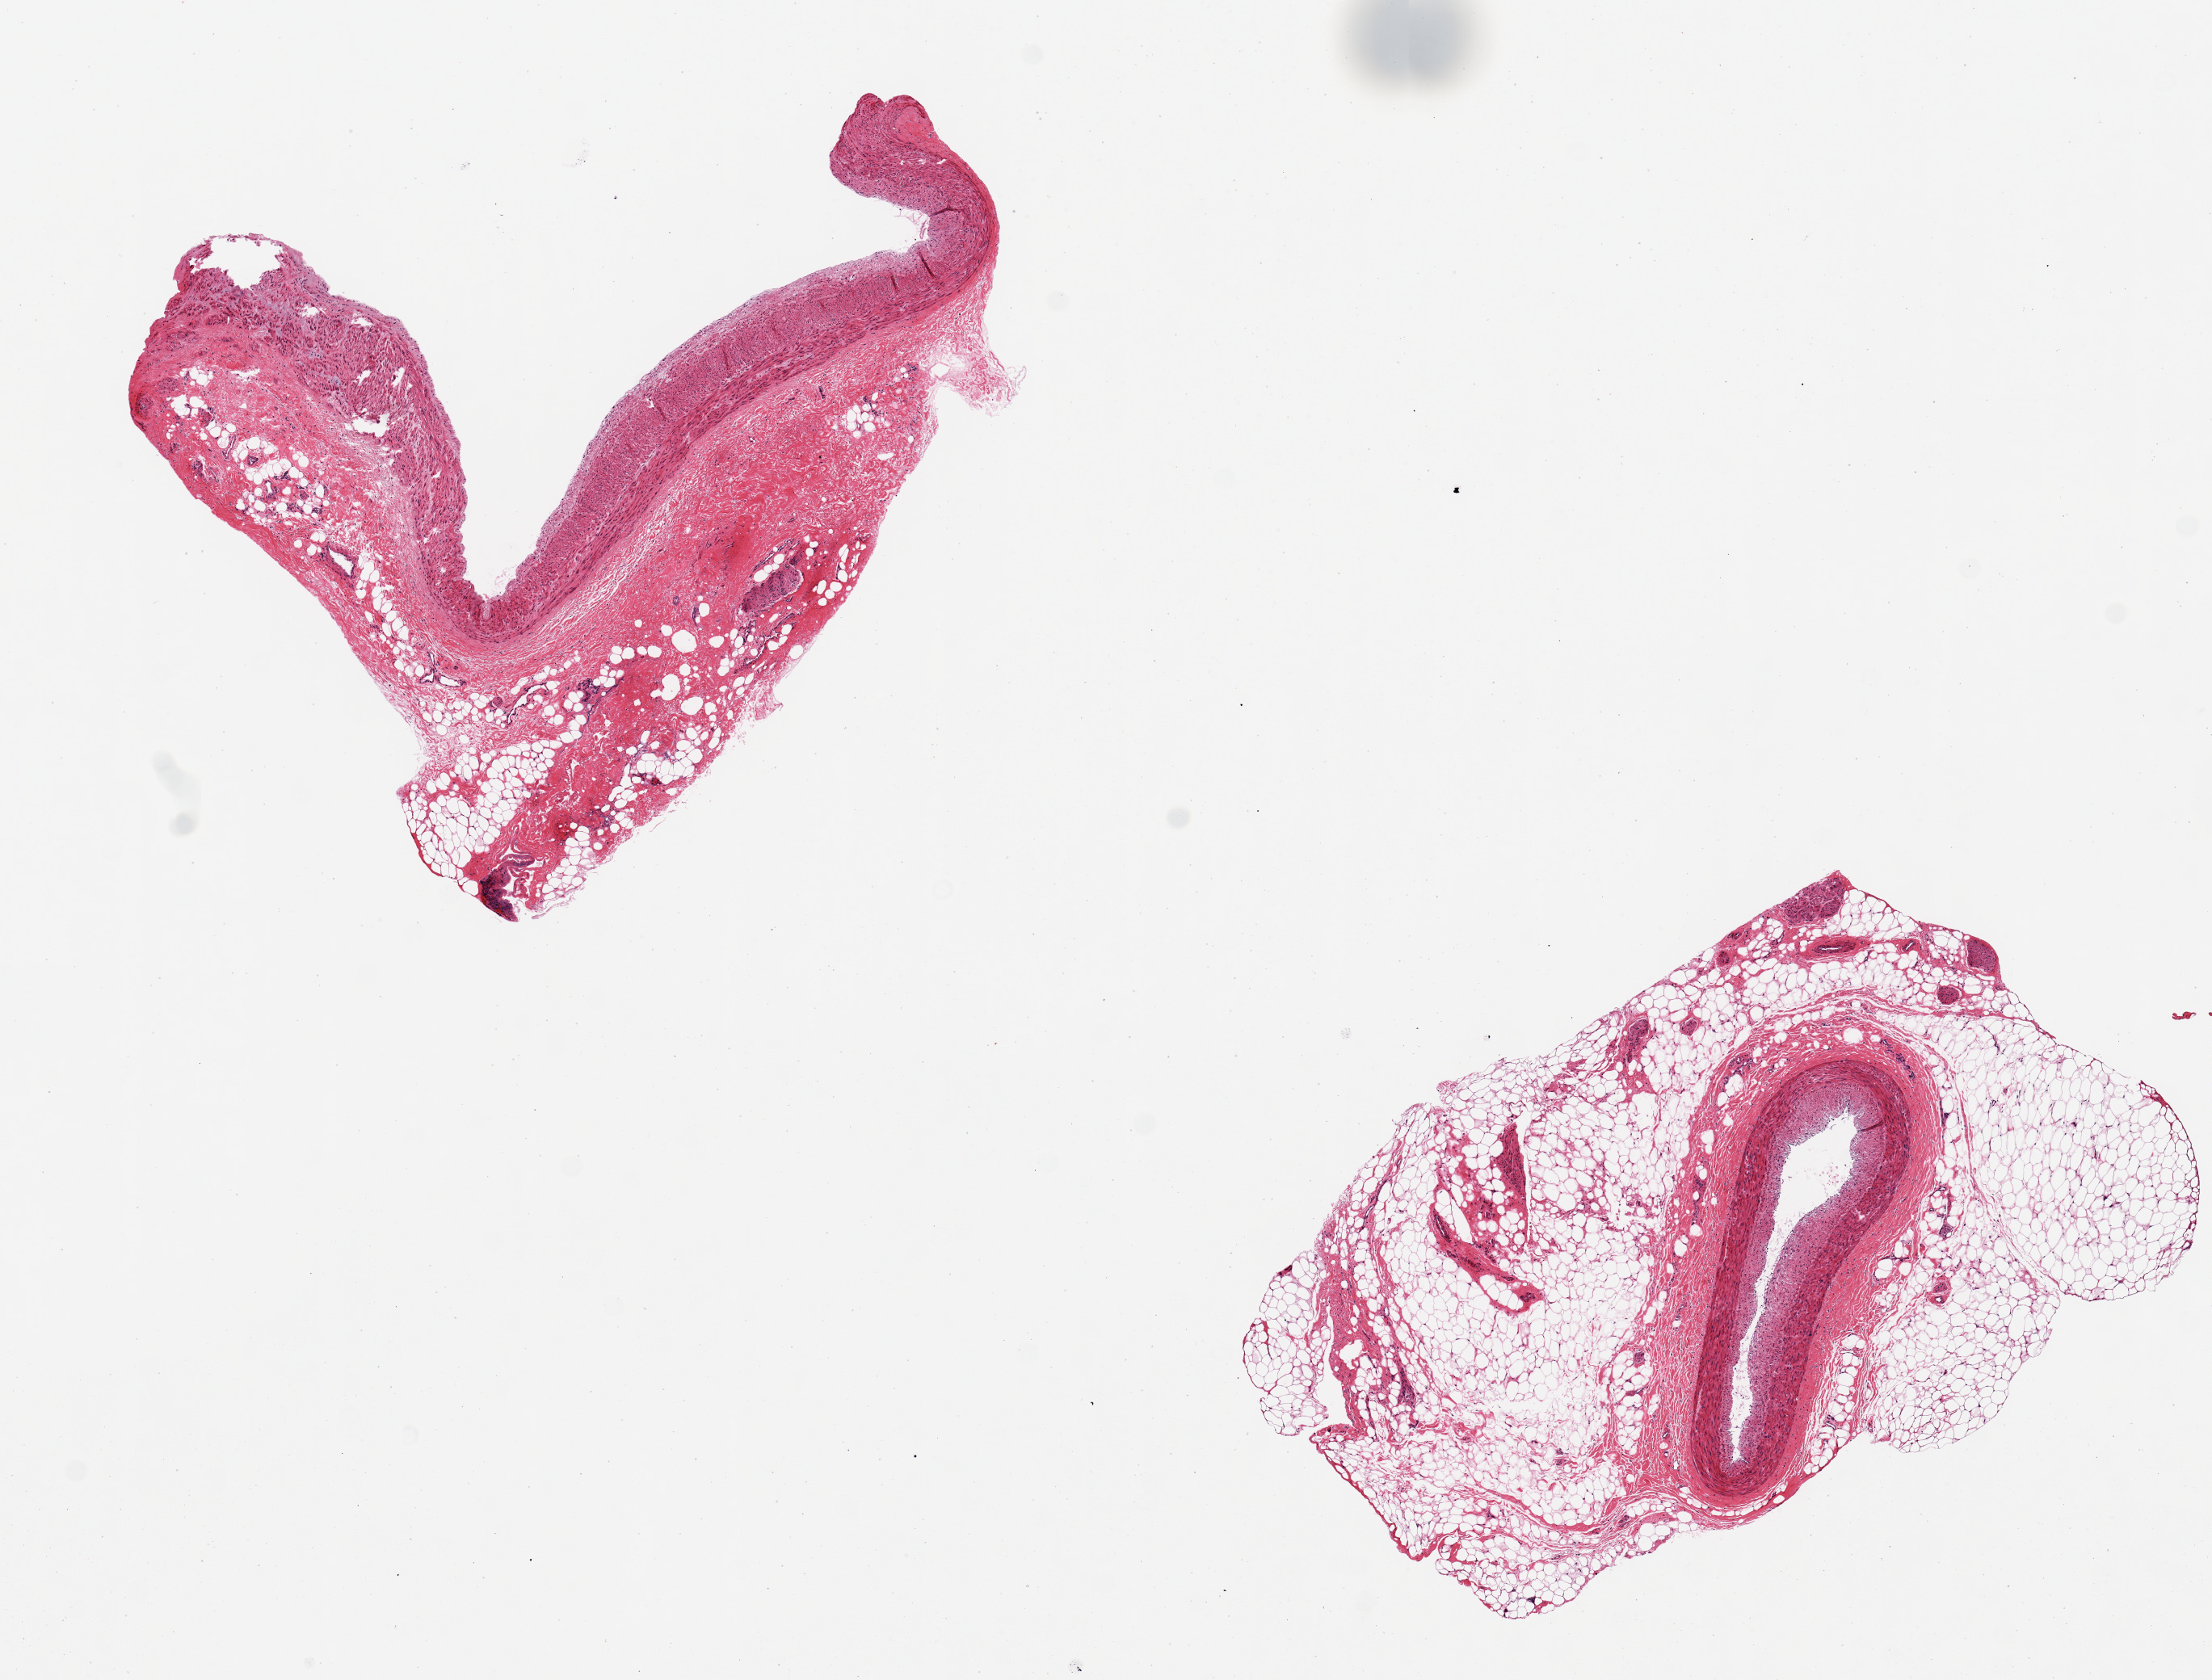
H&E whole-slide image, whole scanned area (about 10.8 x 8.2 mm) shown as a low-resolution overview; PAXgene-fixed paraffin-embedded (PFPE) section; section of coronary artery (target tissue); tissue donor sample. Donor sex: female.
Reviewer comment on this tissue sample: 2 pieces, significant attachment of fat (up to 2mm).